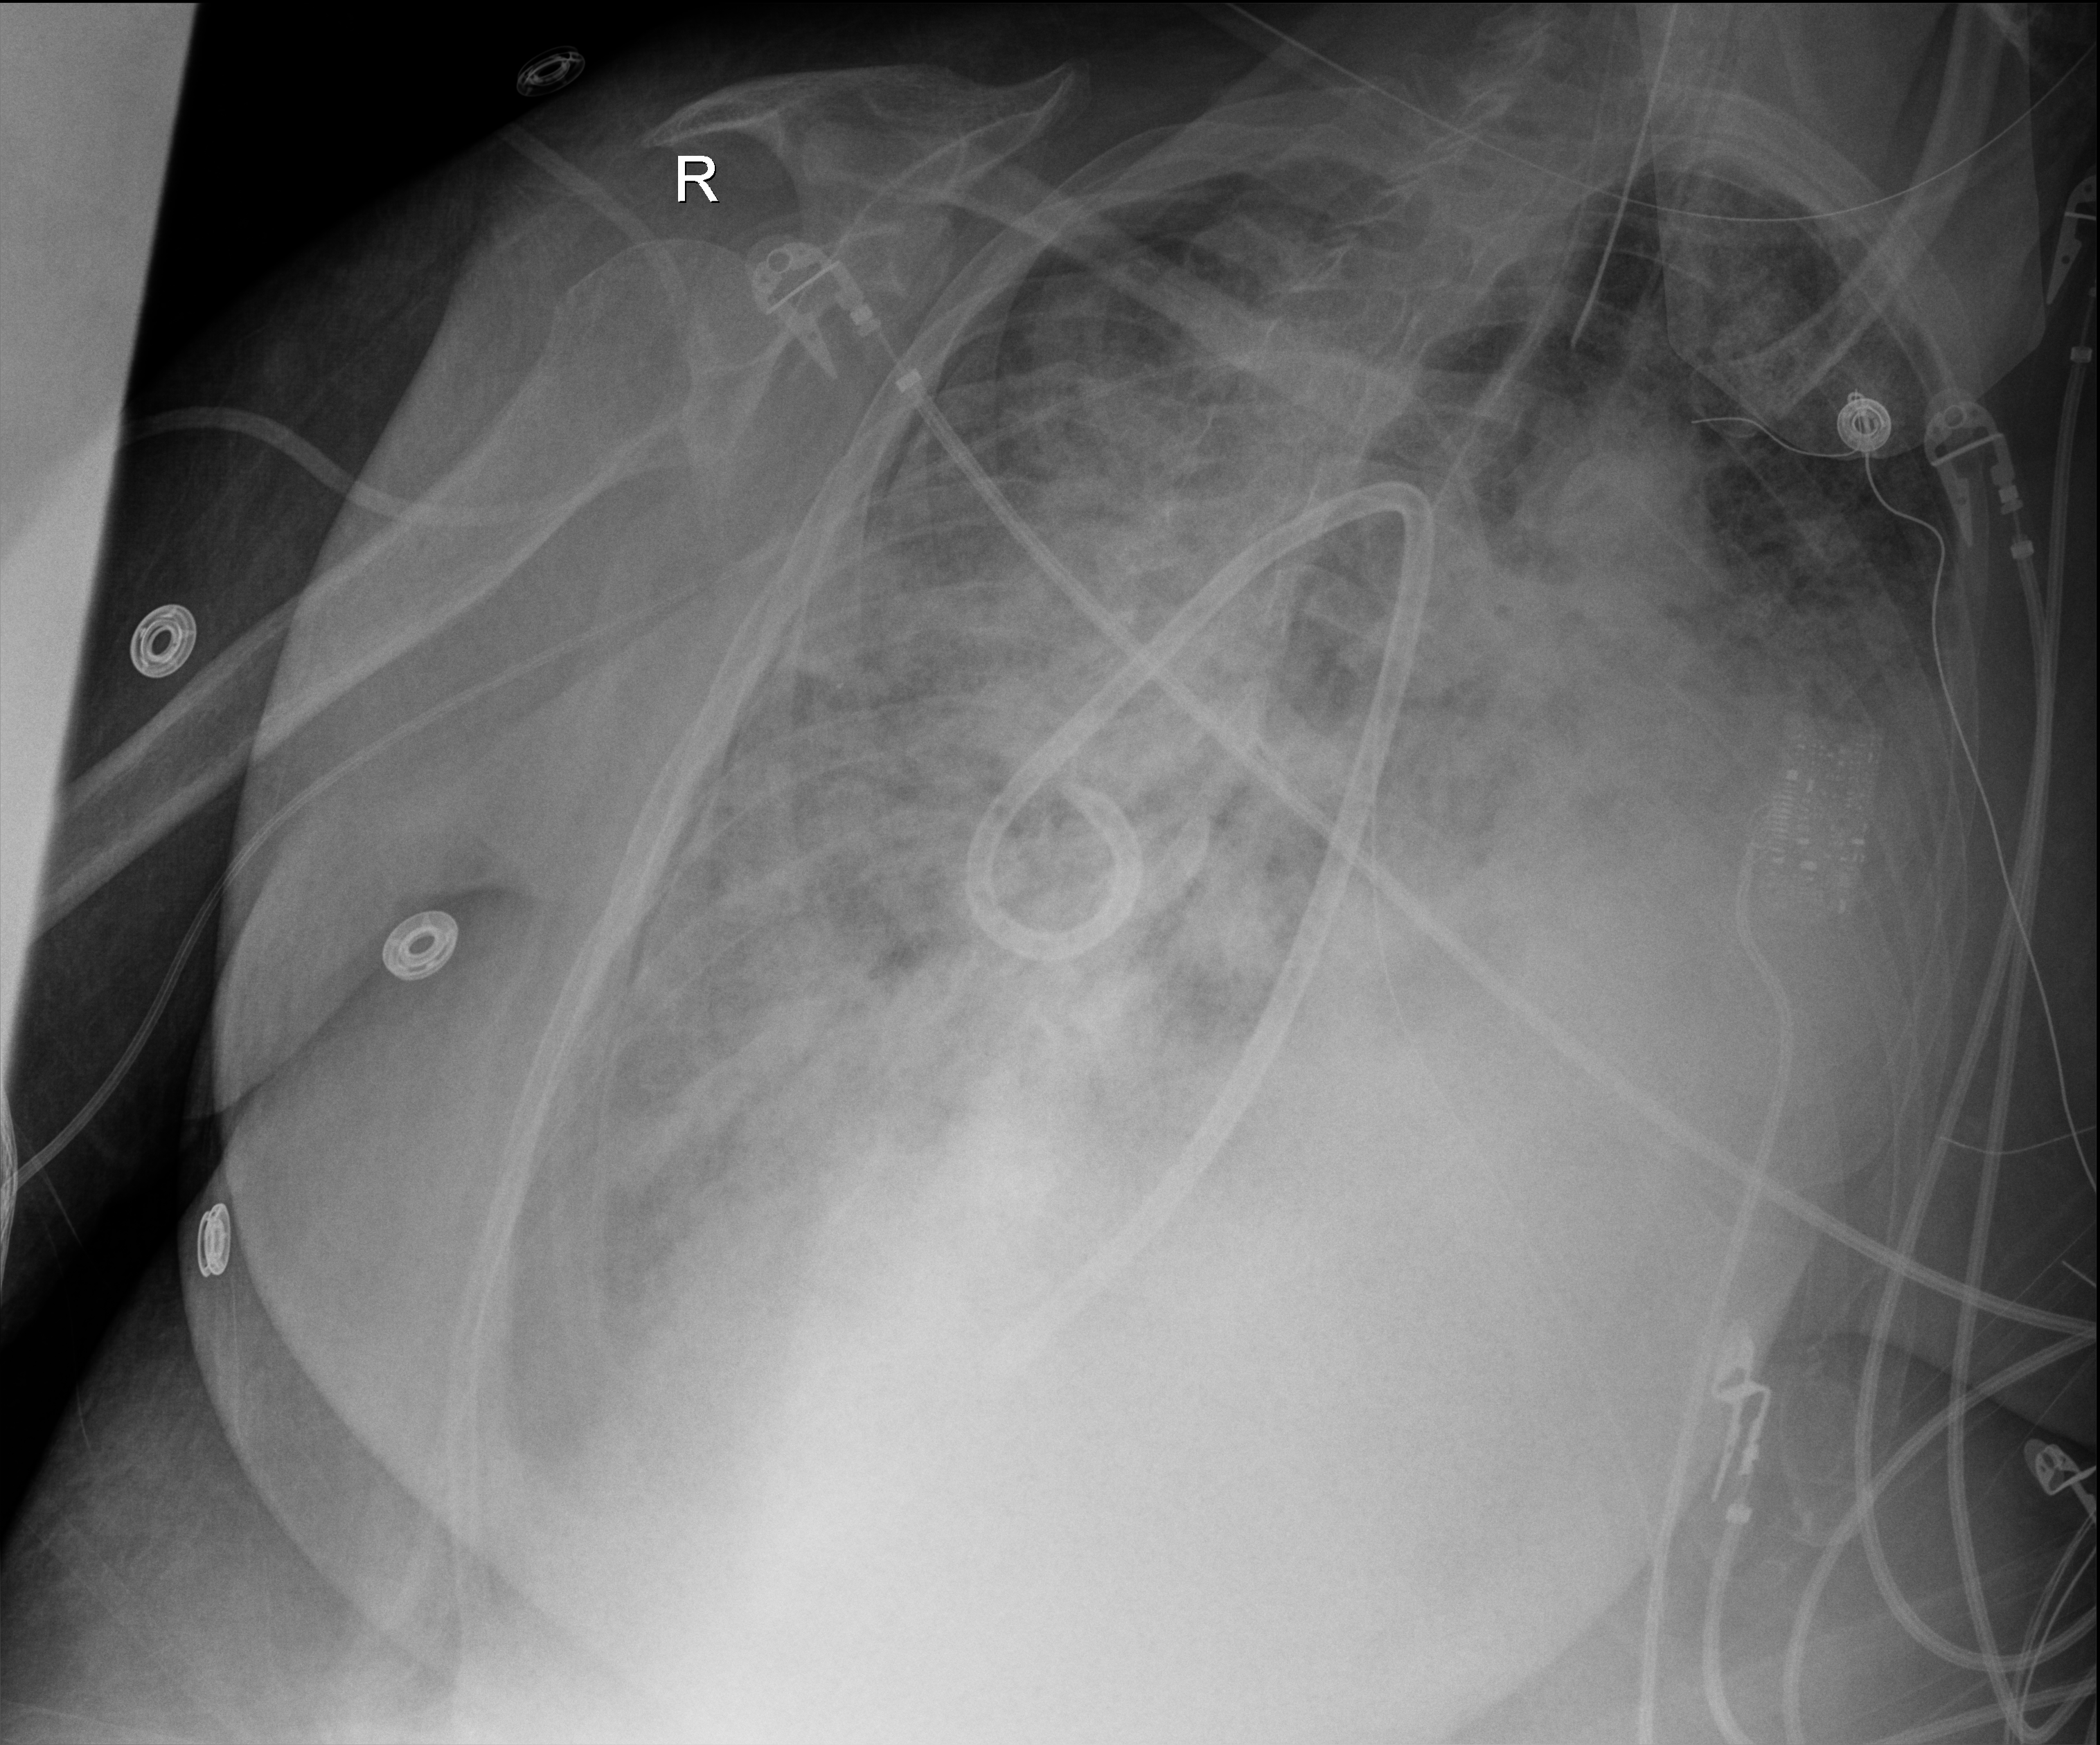
Bedside chest radiograph (digital radiography); anteroposterior (AP) projection. Patient hospitalised with COVID-19, aged 18–59 years.
From the hospital-stay record, not from the radiograph (when in the stay this image was taken is not recorded):
- mechanically ventilated during this hospital stay: yes